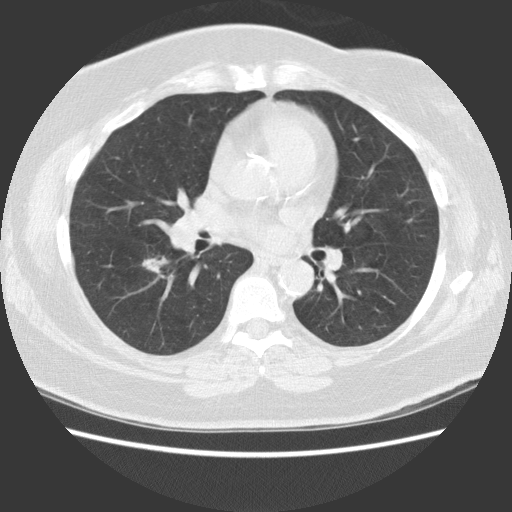
Low-dose screening chest CT, one axial slice; 140 kVp; lung window (W 1500 / L -600 HU); 512 × 512 image matrix, field of view 350 × 350 mm.
Outlined on this slice (manually delineated by an expert):
- lesion 1 (tumor, lower lobe of right lung): bounding box (x1, y1, x2, y2) in pixels: (142, 256, 169, 275)